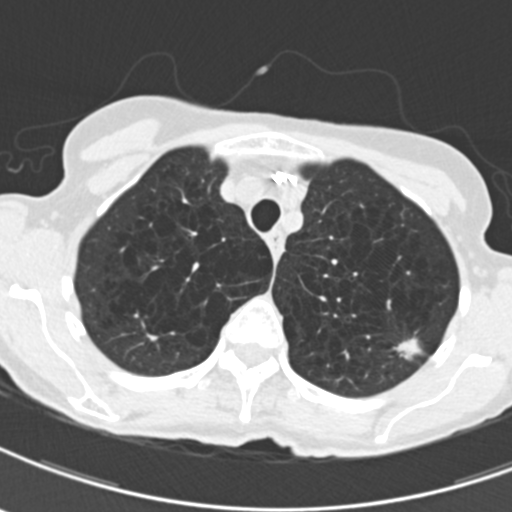
Axial slice from a low-dose chest CT screening exam; third screening round (two years after baseline); lung window (W 1500 / L -600 HU). Female participant, aged 71 years at enrolment.
- Lesion marked by an expert reader, bounding box [x1, y1, x2, y2] px = [390, 325, 437, 368].
- The exam's reader record, not a measurement of the box and not confirmed to be the same lesion: non-calcified nodule or mass ≥4 mm, left upper lobe, 12 × 9 mm, spiculated (stellate) margins, mixed attenuation, pre-existing on the prior screen: yes; interval growth: yes.
- Lung cancer was diagnosed 114 days after this screen: adenocarcinoma, NOS, left upper lobe, moderately differentiated (G2), stage IA (AJCC 6th edition), 12 mm at pathology.